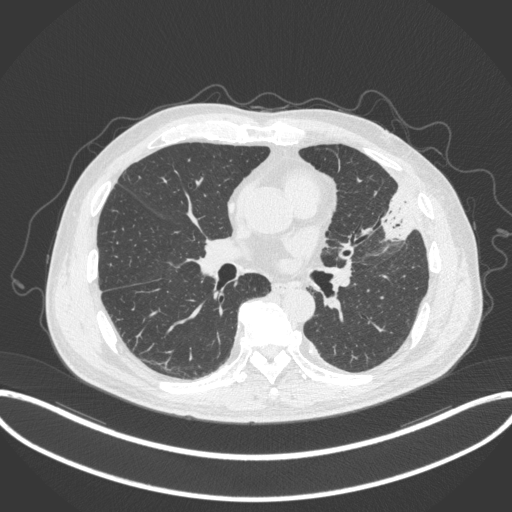
Chest CT, one axial slice; position 170 of 382 along the scan axis; reconstruction kernel B31f; 120 kVp; lung window (W 1500 / L -600 HU); 512 × 512 image matrix, field of view 415 × 415 mm. Patient: male, 64 years. Case-level facts recorded for this patient, not image findings: clinical TNM (as recorded): T4 N1 M0; histopathological grade: G3.
Annotated regions visible in this slice (rectangle marked by the reading radiologist):
- lung tumour (recorded histology: adenocarcinoma): bounding box <378,183,419,246> (left, top, right, bottom; pixels)